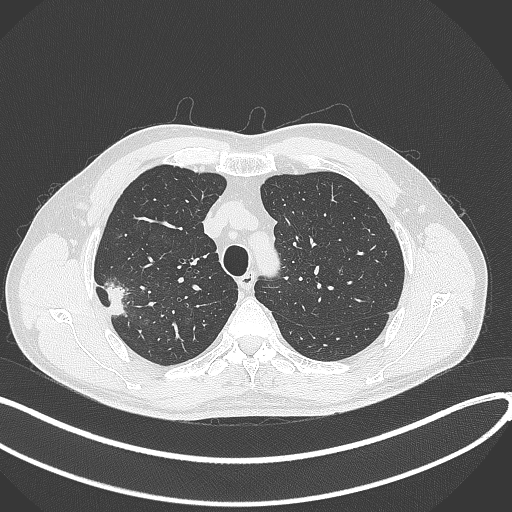
Chest CT, one axial slice; position 326 of 381 along the scan axis; lung window (W 1500 / L -600 HU); 1 mm slice thickness; 512 × 512 image matrix, field of view 400 × 400 mm. Patient: male, 62 years. From the clinical record (not read from this slice): clinical TNM (as recorded): T1c N0 M0; histopathological grade: G2-3.
Outlined on this slice (rectangle marked by the reading radiologist):
- lung tumour (recorded histology: adenocarcinoma): bounding box (x1, y1, x2, y2) in pixels: (101, 282, 128, 321)